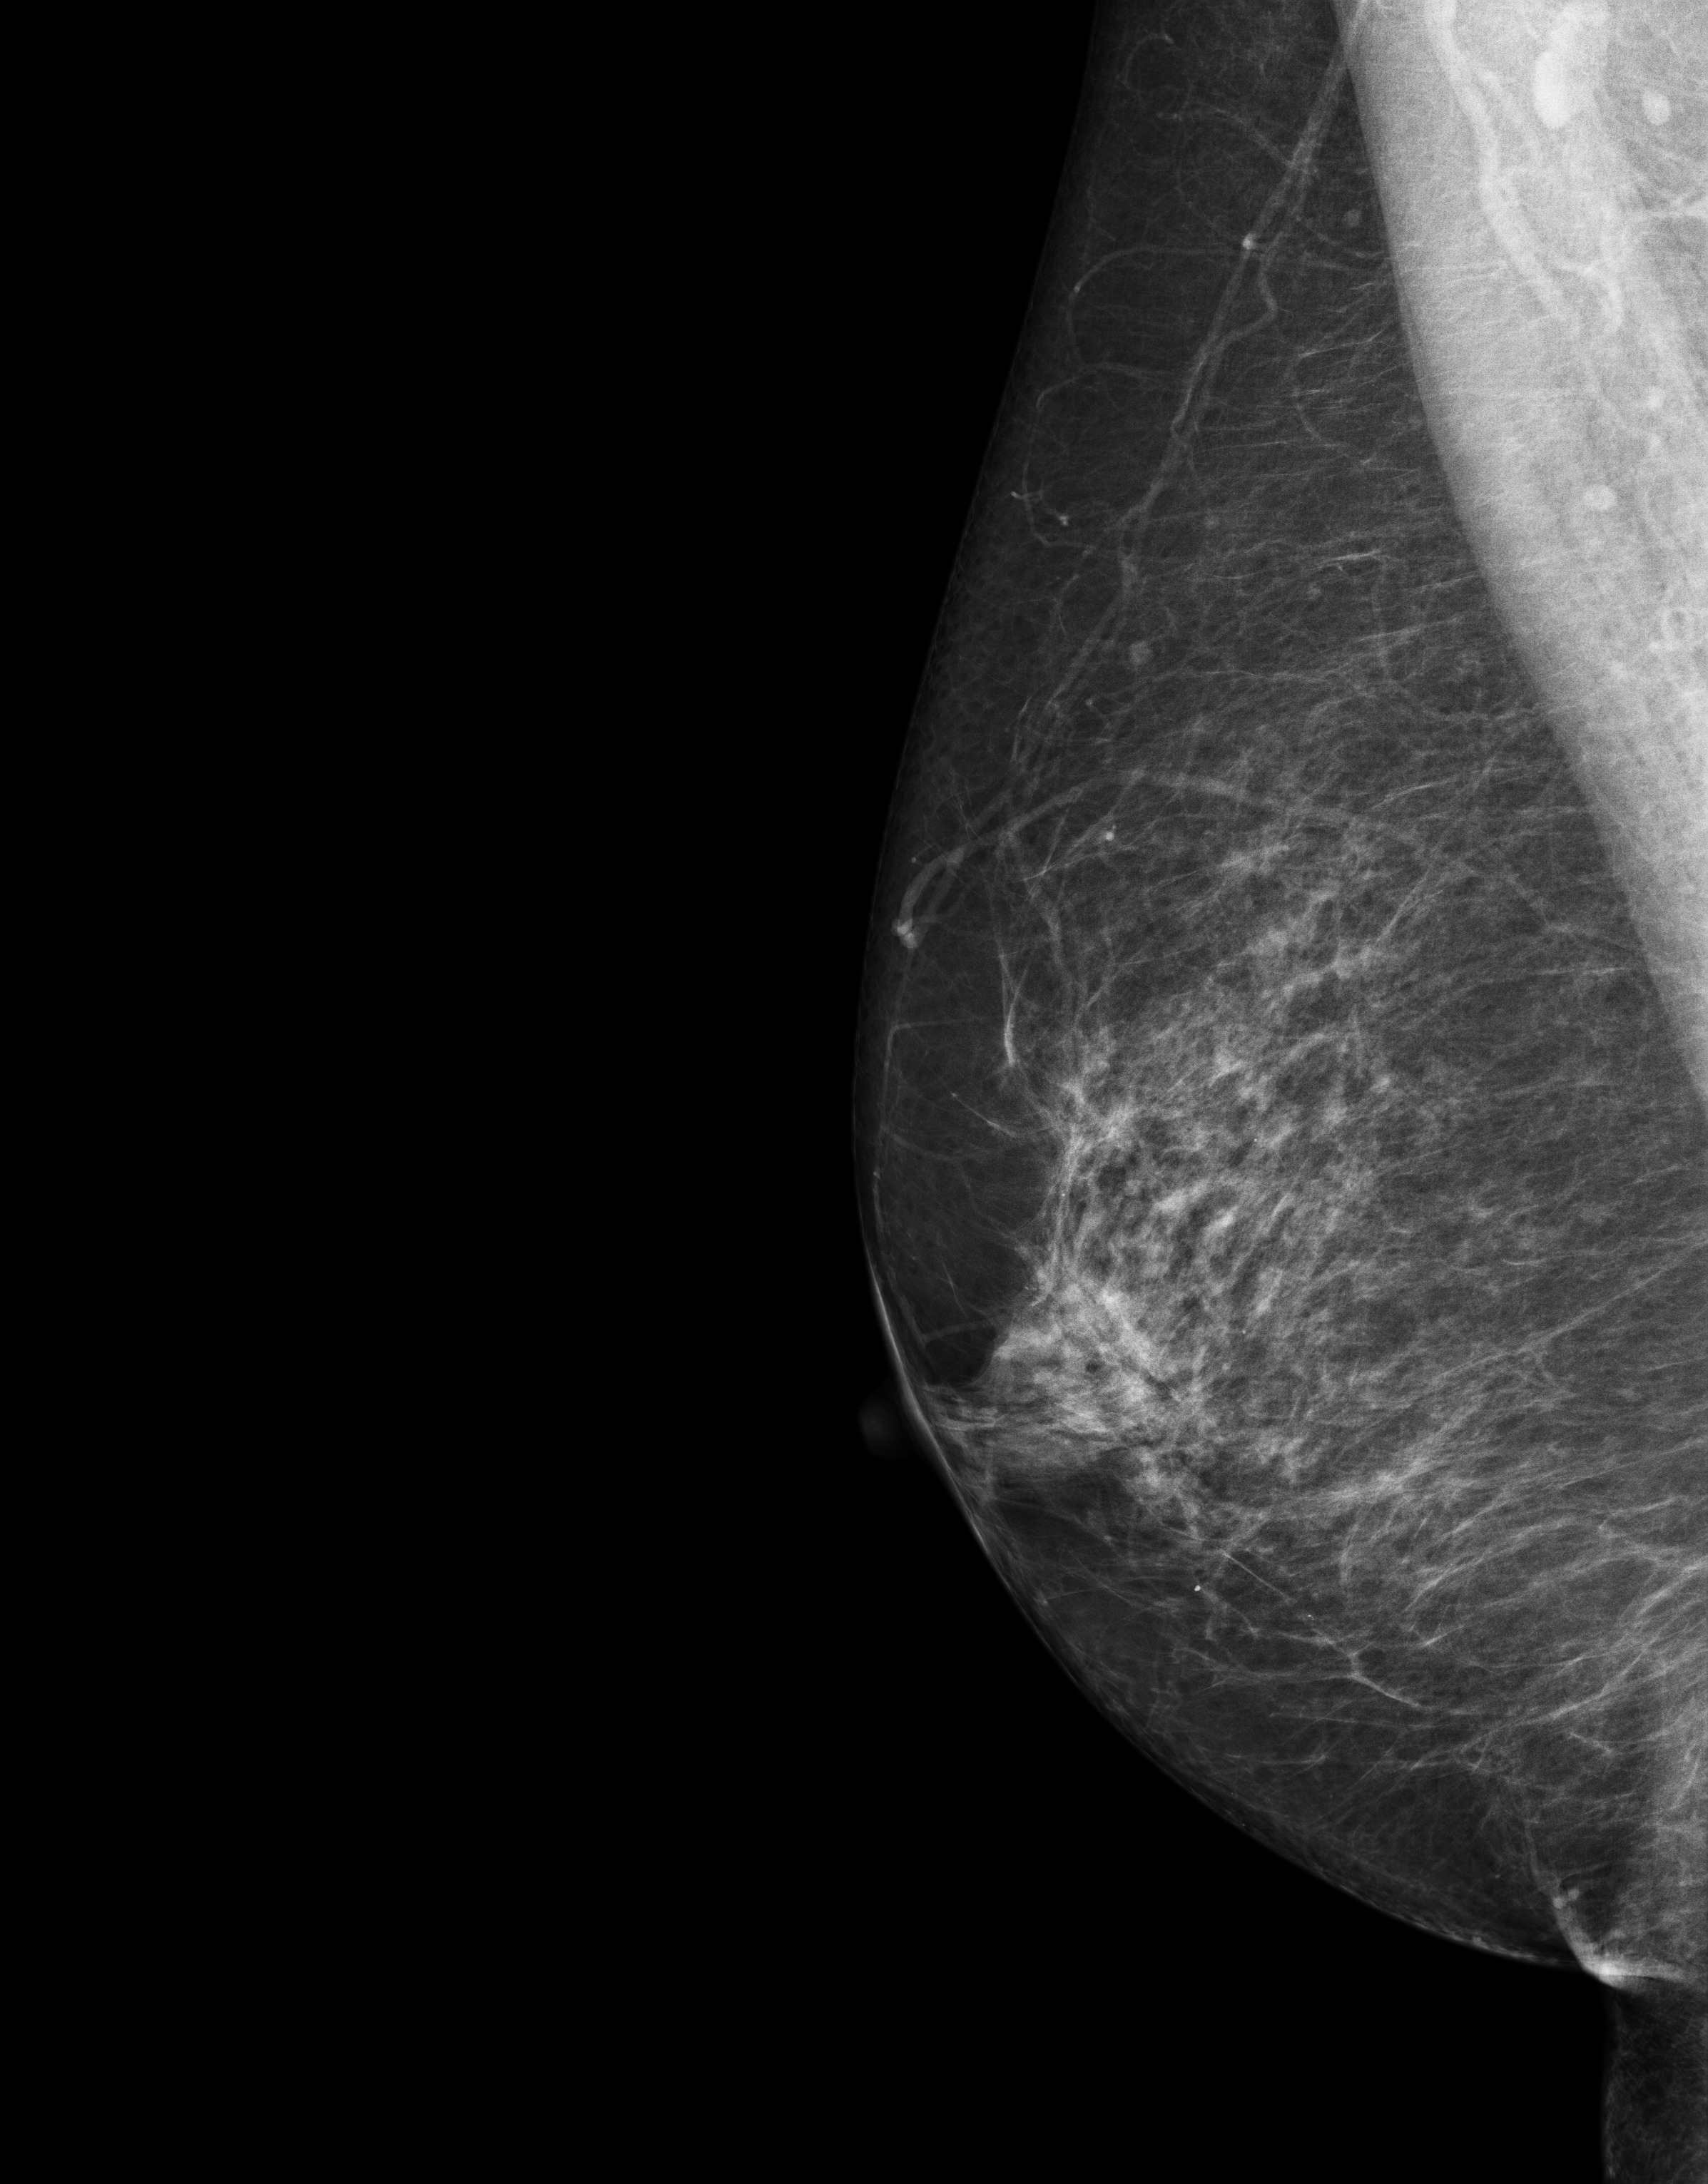
Full-field digital mammogram (FFDM), right breast, medio-lateral oblique projection, screening examination, compressed breast thickness 78 mm, system: Senographe Essential ADS_56.21.3. Female patient, age 53 years.
Final BI-RADS category for the screening round (tomosynthesis exam, both breasts): category 4.